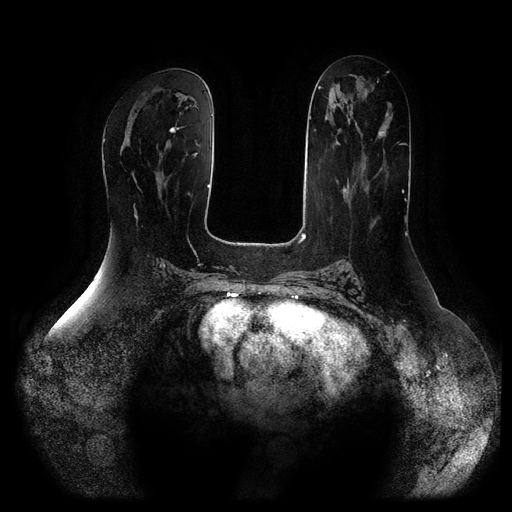
Breast MRI (dynamic contrast-enhanced, multi-phase), one axial slice. Slice 45 of 116 in the series (ordered by position). Dynamic contrast-enhanced series, time point 2 of 5 at this slice position (early post-contrast). 1.5 T. TE 2.5 ms, TR 5.2 ms. 2 mm slice thickness. 512 × 512 image matrix, field of view 400 × 400 mm. Female patient, age 66 years.
Structures marked on this image (semi-automatic segmentation, software-assisted and operator-edited):
- breast lesion (labelled 'tumour' in the annotation; benign lesions carry a separate 'benign' label): bounding box (x1, y1, x2, y2) in pixels: (169, 122, 181, 133)